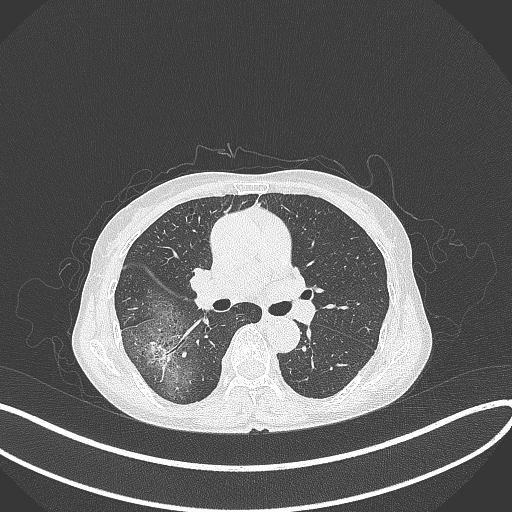
Chest CT, one axial slice. 120 kVp. Lung window (W 1500 / L -600 HU). 1 mm slice thickness. 512 × 512 image matrix, field of view 400 × 400 mm. Female patient, age 69 years. From the clinical record (not read from this slice): clinical TNM (as recorded): T1b N0 M0.
Structures marked on this image (rectangle marked by the reading radiologist):
- lung tumour (recorded histology: adenocarcinoma): bounding box <139,334,177,375> (left, top, right, bottom; pixels)